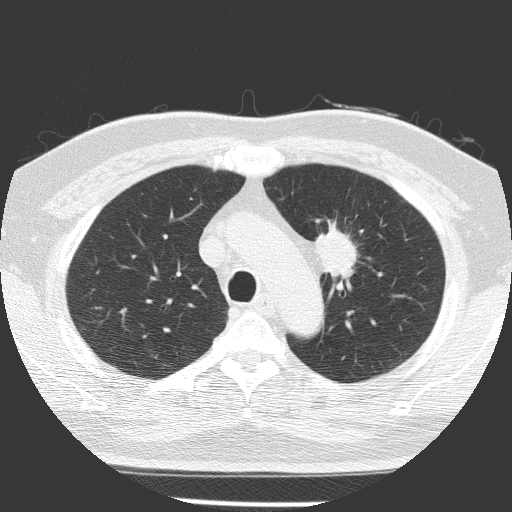
Low-dose screening chest CT, one axial slice; slice 113 of 156 in the series (ordered by position); reconstruction kernel FC51; 120 kVp; lung window (W 1500 / L -600 HU); 512 × 512 image matrix.
Outlined on this slice (expert manual segmentation):
- lesion 1 (tumor, upper lobe of left lung): bounding box [x1, y1, x2, y2] px = [315, 225, 358, 280]